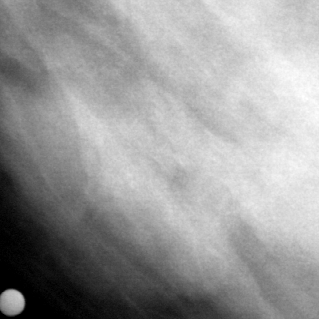
Crop from a digitized film mammogram around one marked abnormality, right breast, CC view.
Marked abnormality: mass, shape oval, margins obscured; BI-RADS assessment category 4; pathology (as recorded): malignant.